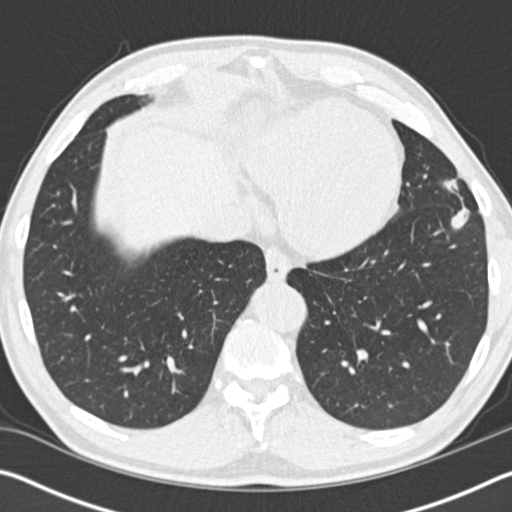
Low-dose screening chest CT, one axial slice. Slice 40 of 162 in the series (ordered by position). Reconstruction kernel B30f. 120 kVp. Lung window (W 1500 / L -600 HU). 512 × 512 image matrix, field of view 340 × 340 mm.
Structures marked on this image (expert manual segmentation):
- lesion 1 (tumor, upper lobe of left lung): box from (x=443, y=179) to (x=470, y=230) px